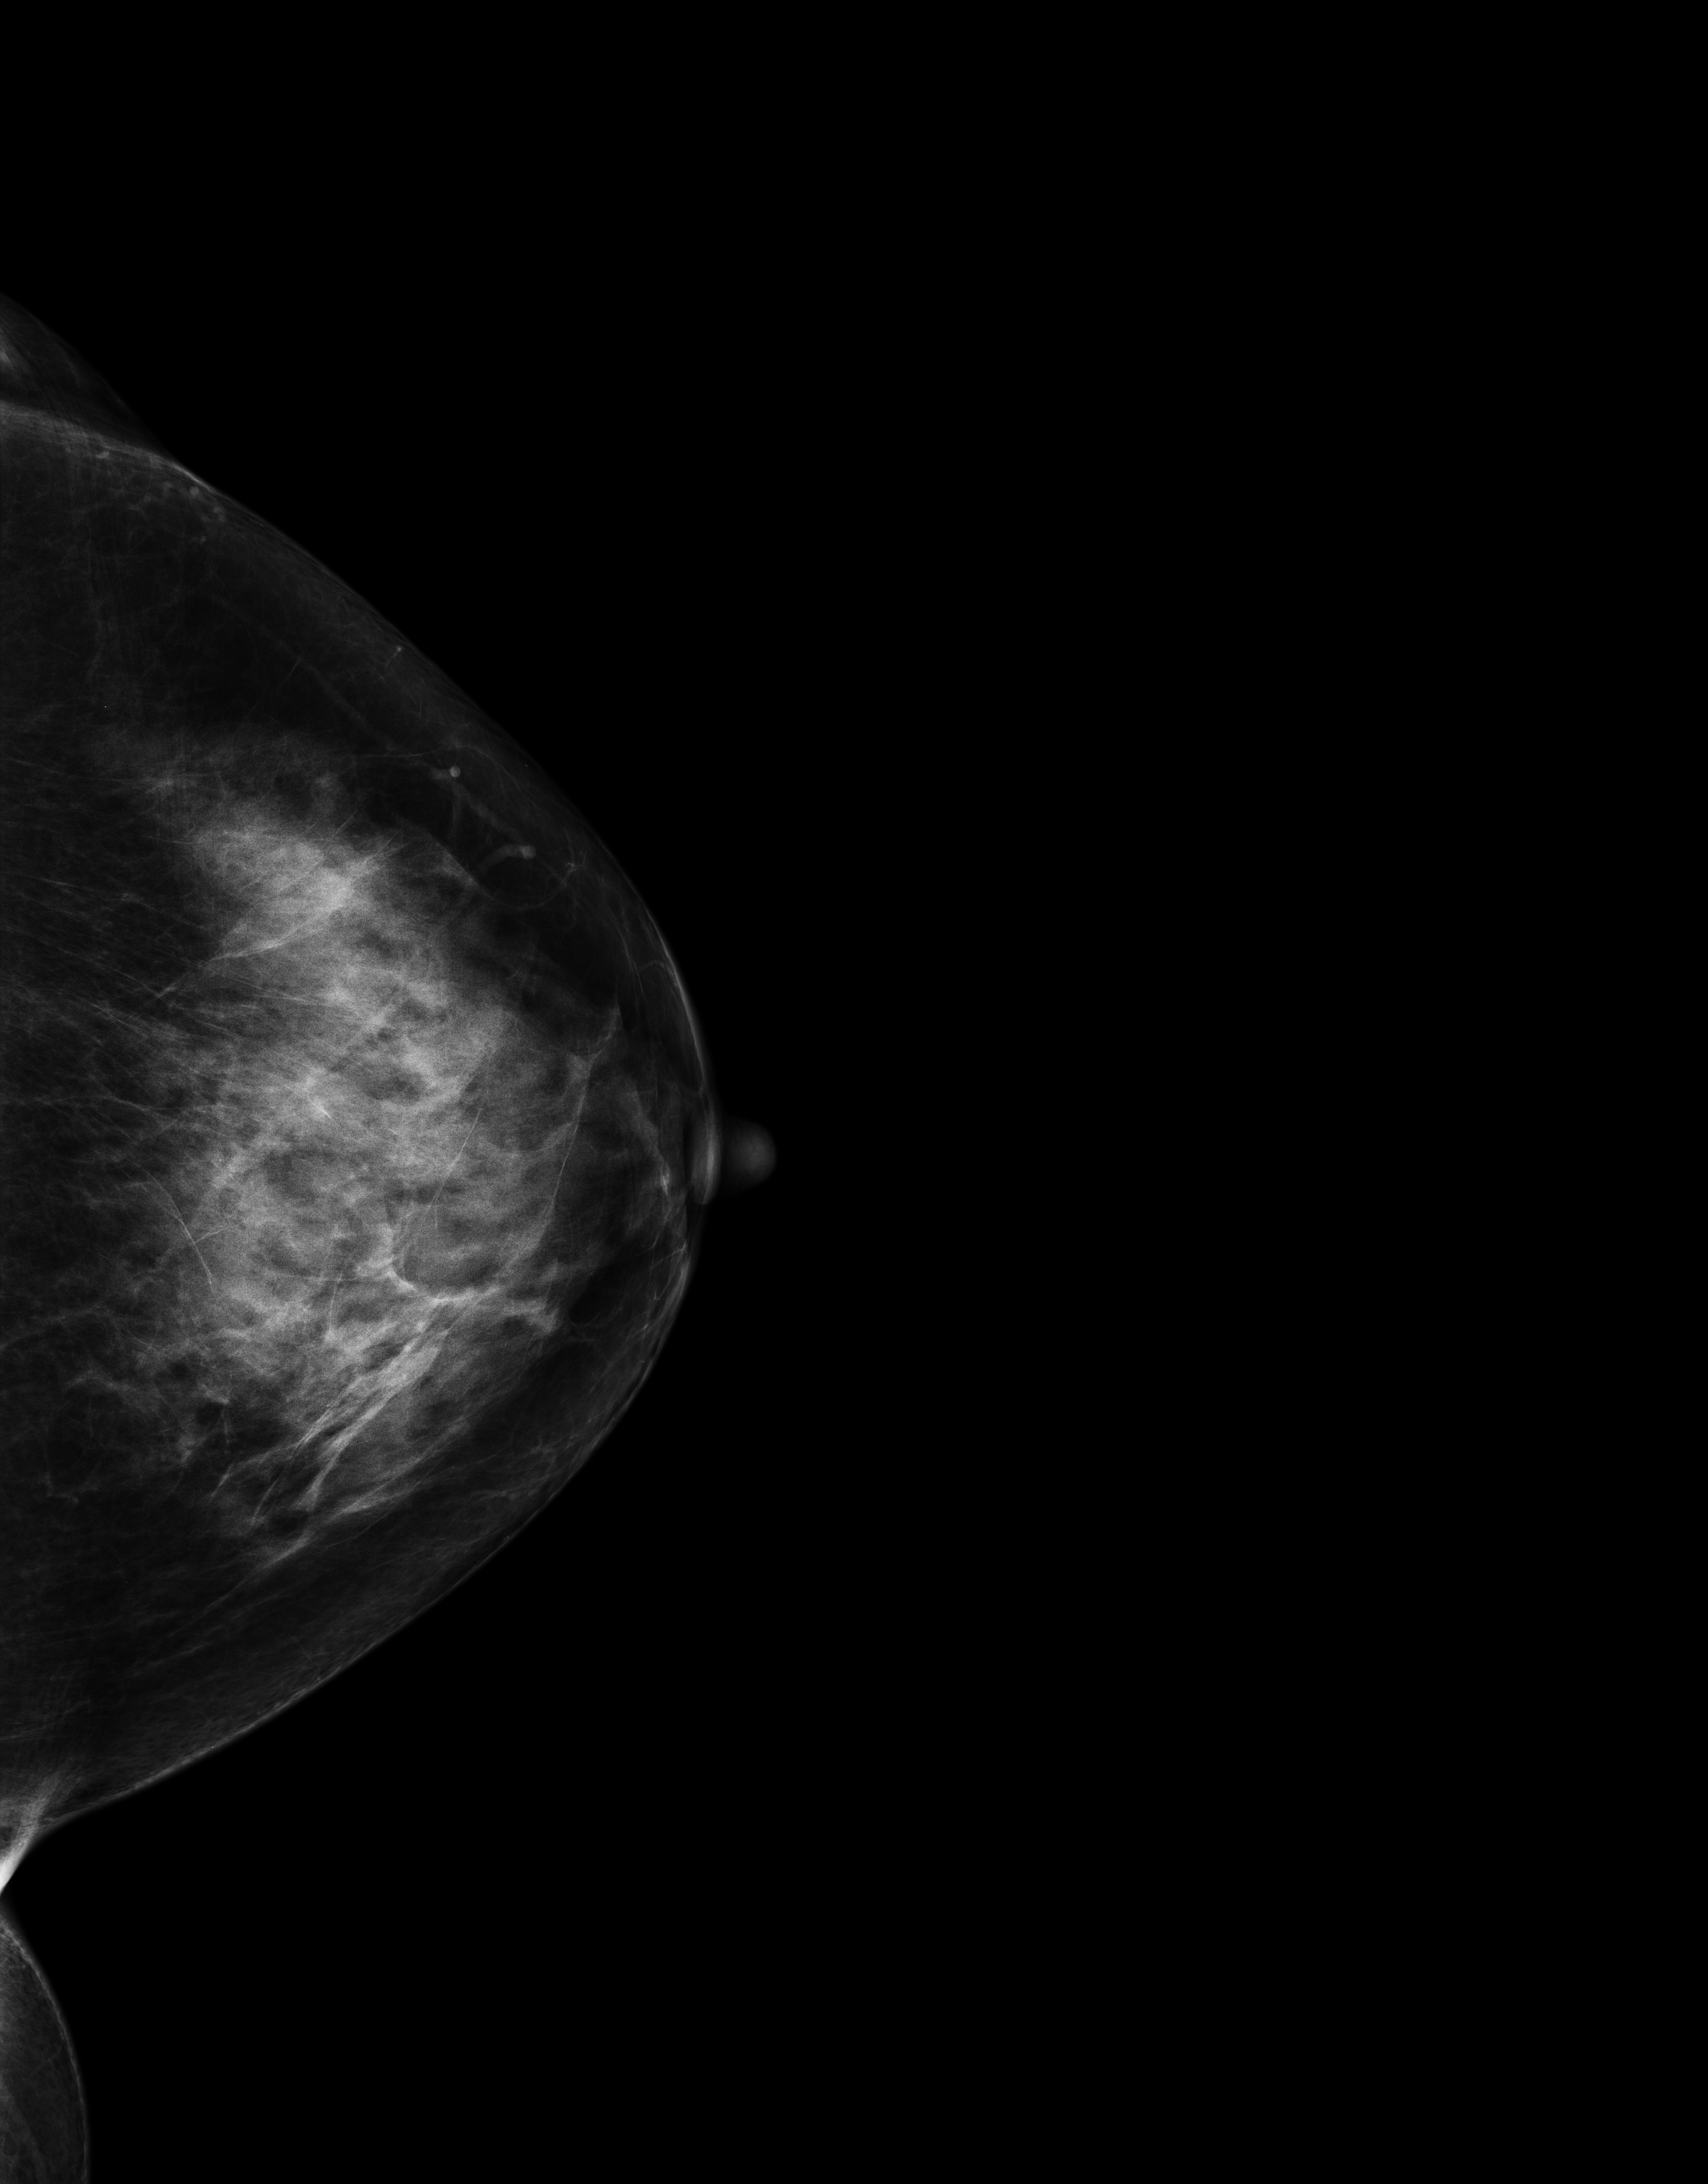
Digital mammogram (FFDM); left breast; cranio-caudal projection; screening examination; compressed breast thickness 61 mm; system: Senographe Essential ADS_56.21.3. Patient aged 67 years (female).
Breast density at the screening exam (both breasts): heterogeneously dense (BI-RADS density category c). Final BI-RADS category for the screening round (tomosynthesis exam, both breasts): category 1. Recall: no recall after this screen.